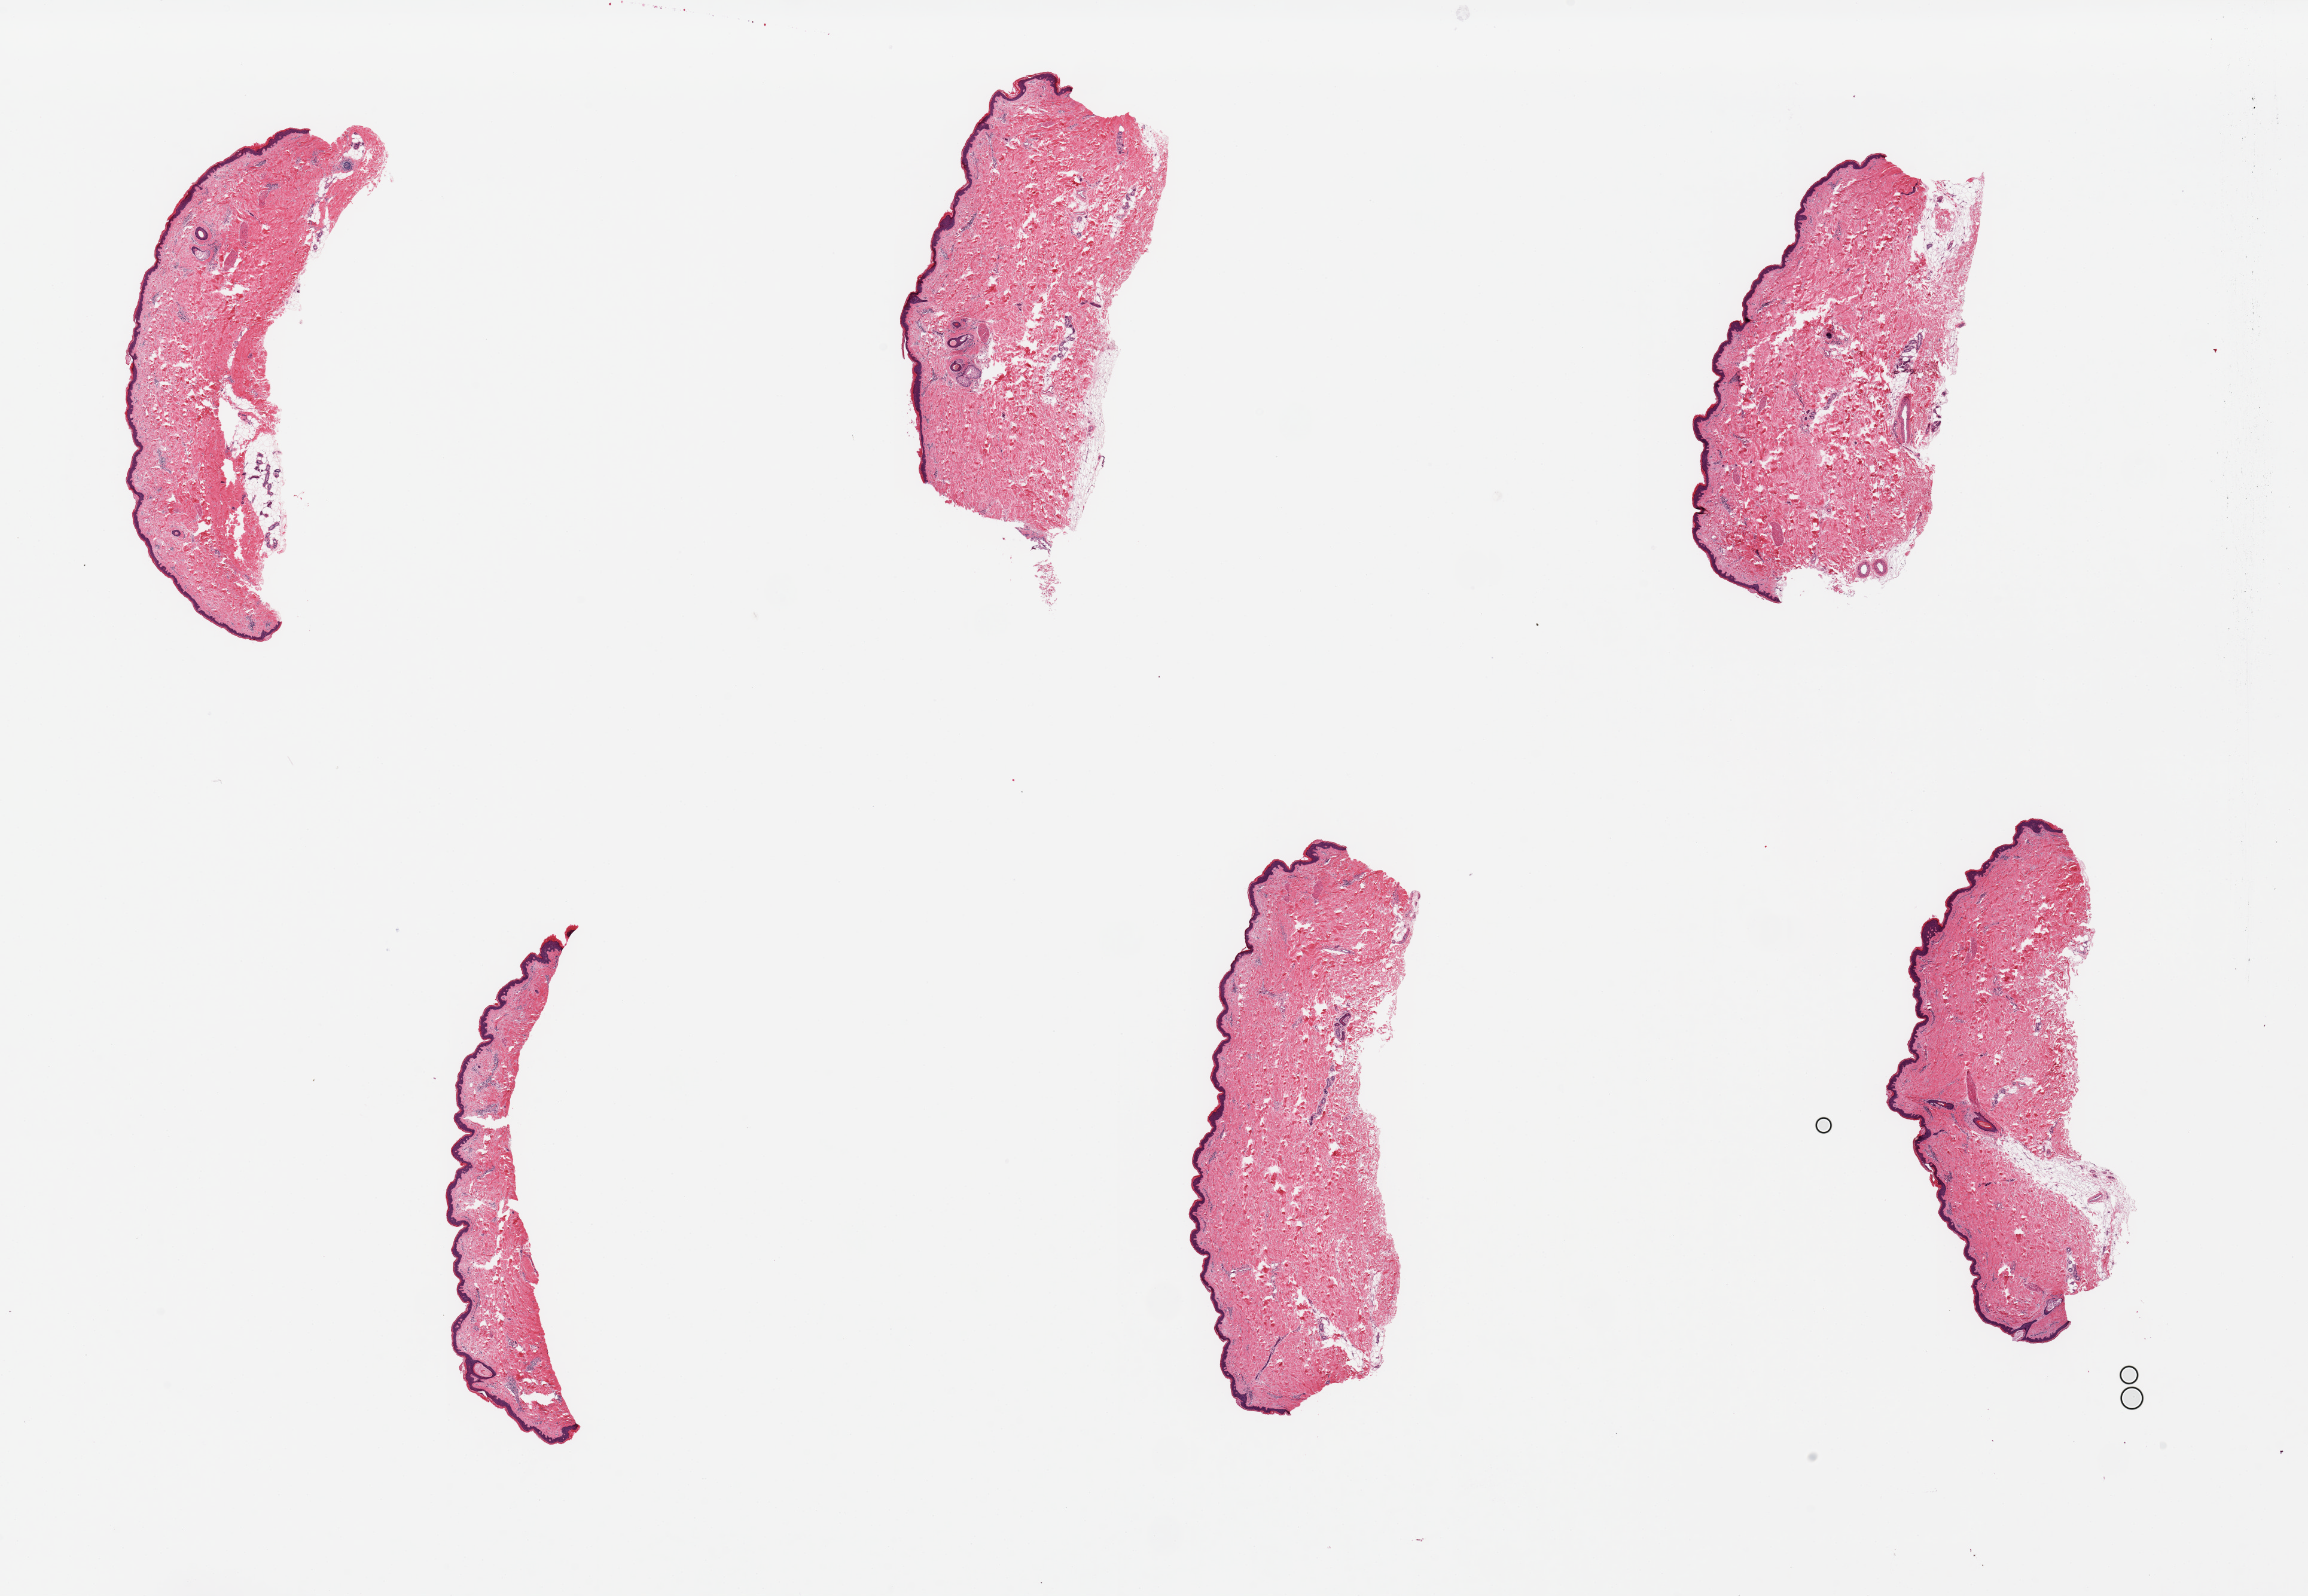
Digitized hematoxylin and eosin (H&E)-stained section, low-resolution overview of the scanned area, about 30.5 x 21.1 mm. PAXgene-fixed, paraffin-embedded tissue. Section of skin of lower leg (target tissue). Tissue donor sample. Donor: male.
Review note (as recorded): 6 pieces, 7x3mm; largely free of subcutaneous adipose.